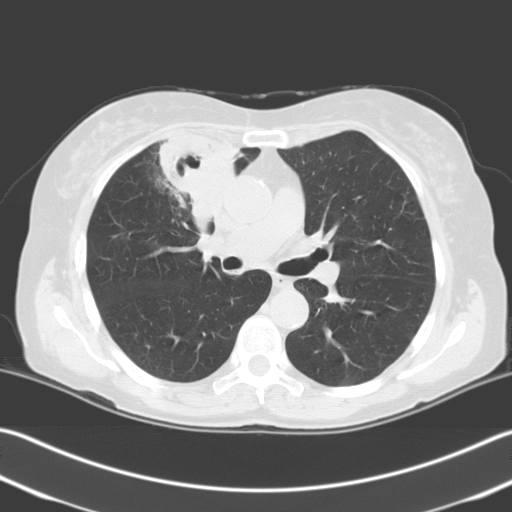
Low-dose screening chest CT, one axial slice. 140 kVp. Lung window (W 1500 / L -600 HU). 3.2 mm slice thickness. 512 × 512 image matrix.
Annotated regions visible in this slice (manually delineated by an expert):
- lesion 1 (tumor, upper lobe of right lung): bounding box [x1, y1, x2, y2] px = [159, 133, 242, 231]